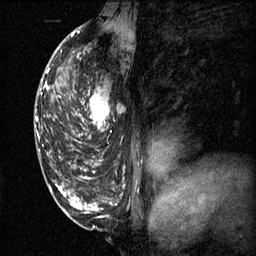
Breast MRI (dynamic contrast-enhanced), one sagittal slice; position 33 of 60 along the scan axis; 3 images stored at this slice position (order not interpretable as contrast timing); 1.5 T; TE 4.2 ms, TR 11.1 ms; 256 × 256 image matrix, field of view 180 × 180 mm. Patient: female, 50 years.
Annotated regions visible in this slice (semi-automatically segmented with operator editing):
- analysis volume of interest (the breast-tissue region the enhancement analysis was run in; not a lesion): bounding box (x1, y1, x2, y2) in pixels: (68, 68, 120, 141)
- tumour enhancement mask (voxels above the 70 % enhancement threshold inside the analysis volume of interest): (68, 86, 110, 141)